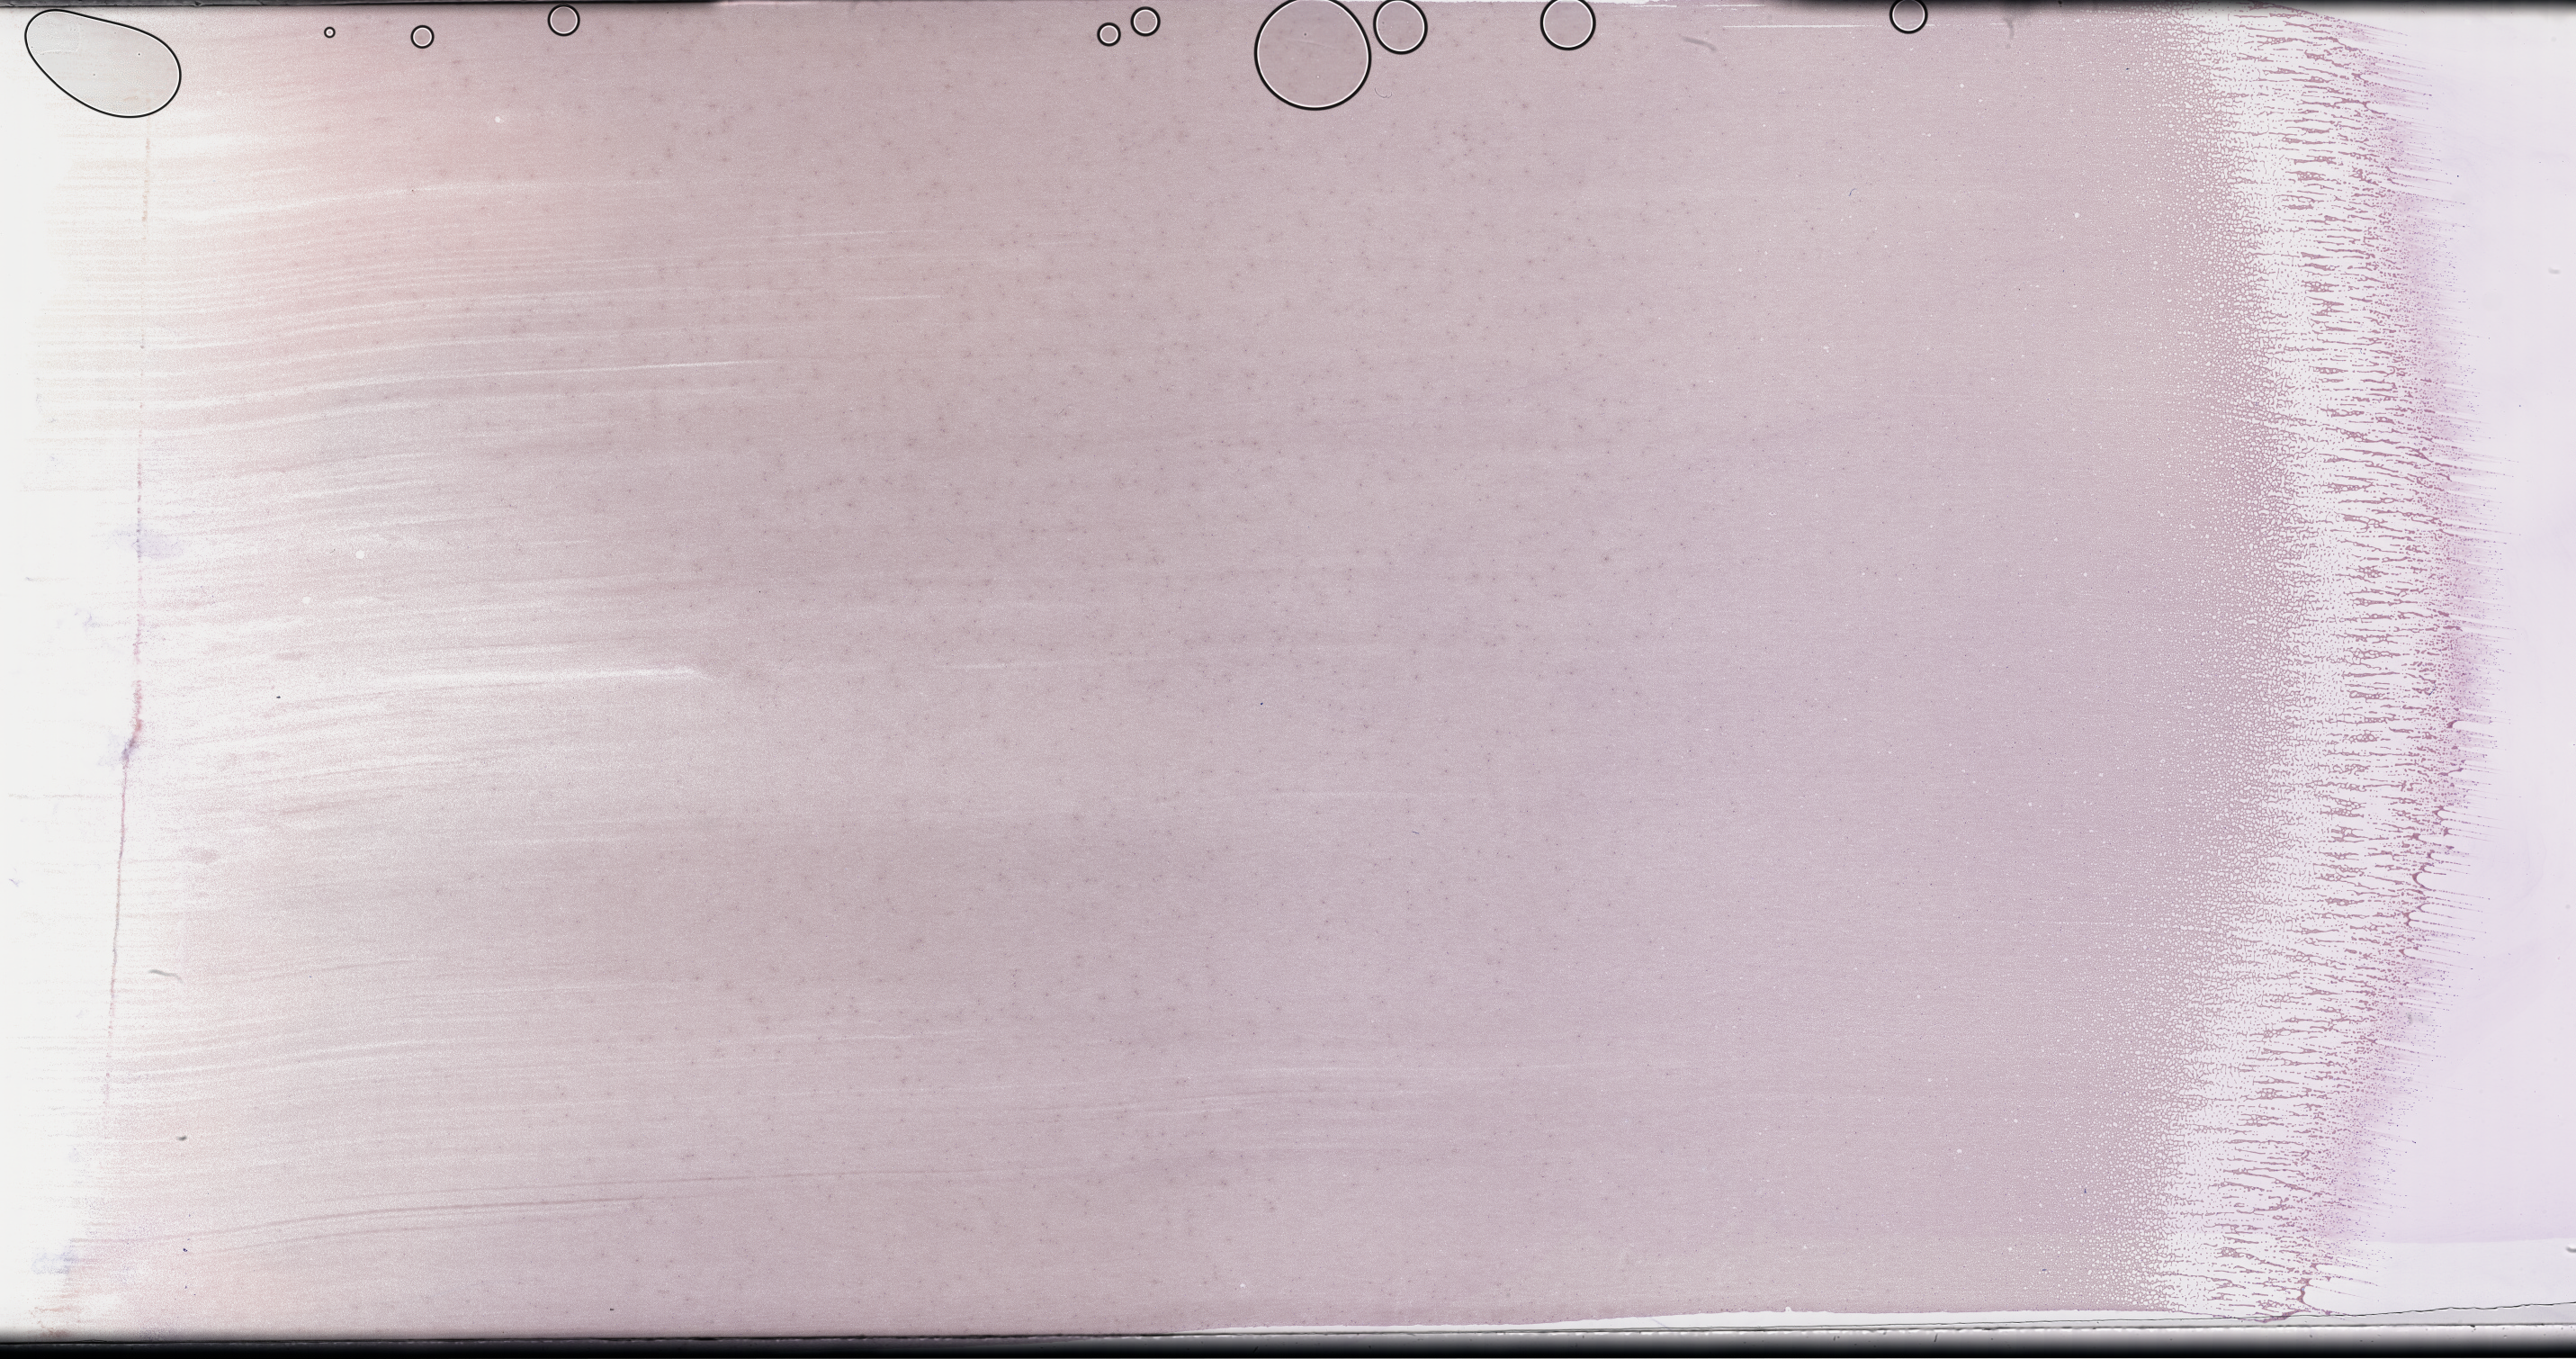
Whole-slide image of a whole blood smear, Wright–Giemsa stain — shown as a low-resolution overview of the whole scanned area (about 46.2 x 24.4 mm), EDTA-anticoagulated smear. Female patient.
Patient diagnosis: Plasma Cell Myeloma.